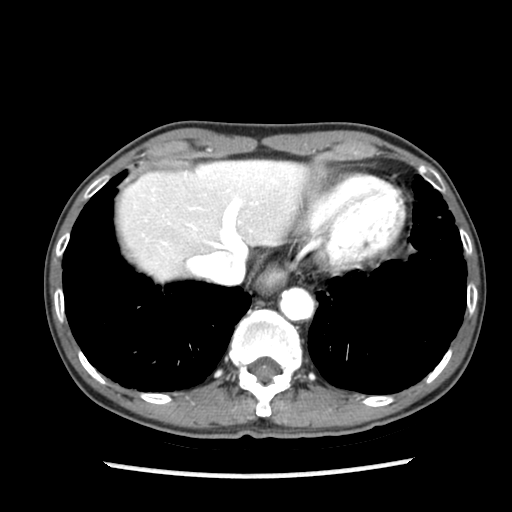
Contrast-enhanced abdominal CT (liver protocol), one axial slice. Slice 71 of 87 in the series (ordered by position). Reconstruction kernel STANDARD. Soft-tissue window (W 400 / L 40 HU). 2.5 mm slice thickness. 512 × 512 image matrix, field of view 300 × 300 mm. From the clinical record (not read from this slice): diagnosis: hepatocellular carcinoma (patient treated with transarterial chemoembolisation; whether this scan precedes or follows treatment is not stated here); TNM stage (as recorded): Stage-IIIB; Child-Pugh class: A; tumour nodularity: uninodular.
Annotated regions visible in this slice (semi-automatic segmentation, software-assisted and operator-edited):
- liver parenchyma outside the tumour (the mass and vessels are separate outlines, so this box may not span the whole liver): box from (x=118, y=160) to (x=315, y=280) px
- liver vessels: (x=164, y=164)–(x=273, y=247)